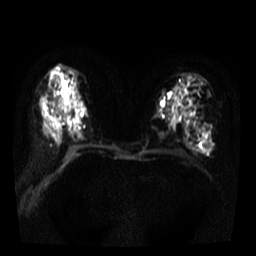
Breast MRI, one axial slice. Position 19 of 38 along the scan axis. Diffusion-weighted series; image 2 of 4 stored at this slice position (different b-values; order by instance number). 3 T. 5 mm slice thickness. 256 × 256 image matrix, field of view 320 × 320 mm. Female patient.
Outlined on this slice (expert manual segmentation):
- tumour on diffusion-weighted imaging: bounding box [x1, y1, x2, y2] px = [202, 140, 207, 151]